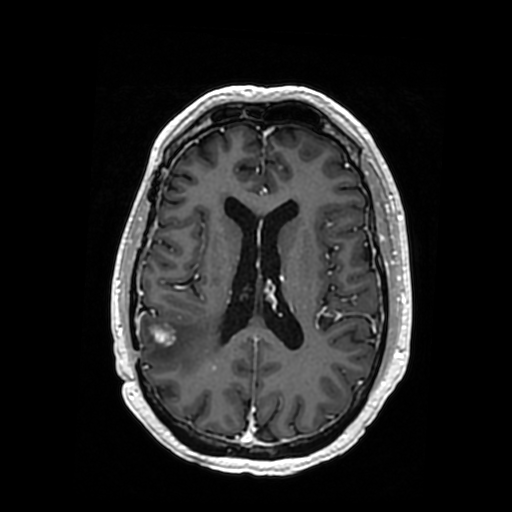
Brain MRI from a brain-tumour surgery series, one axial slice; position 156 of 364 along the scan axis; T1-weighted post-contrast; 0.5 mm slice thickness; 512 × 512 image matrix, field of view 260 × 260 mm. Case-level facts recorded for this patient, not image findings: histopathology: Oligodendroglioma; WHO grade: 3; IDH mutation: yes; tumour location: Right Posterior Temporal Inferior Parietal.
Annotated regions visible in this slice (manually delineated by an expert):
- tumour: bounding box <180,325,214,370> (left, top, right, bottom; pixels)